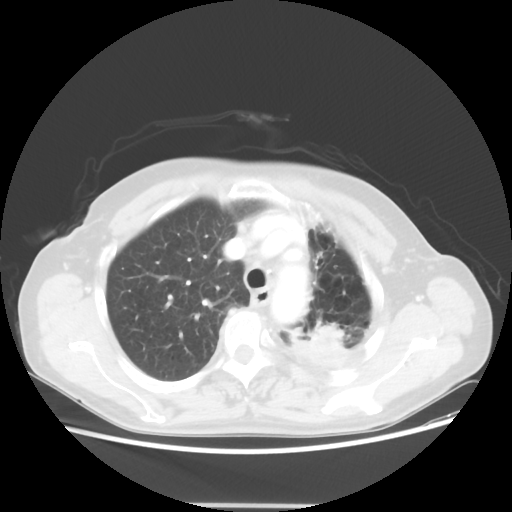
Chest CT, one axial slice. Slice 41 of 56 in the series (ordered by position). Reconstruction kernel STANDARD. 100 kVp. Lung window (W 1500 / L -600 HU). 512 × 512 image matrix, field of view 377 × 377 mm. Female patient, age 63 years. From the clinical record (not read from this slice): clinical TNM (as recorded): T2a N0 M0.
Annotated regions visible in this slice (bounding box drawn by a radiologist):
- lung tumour (recorded histology: adenocarcinoma): bounding box [x1, y1, x2, y2] px = [295, 321, 346, 368]